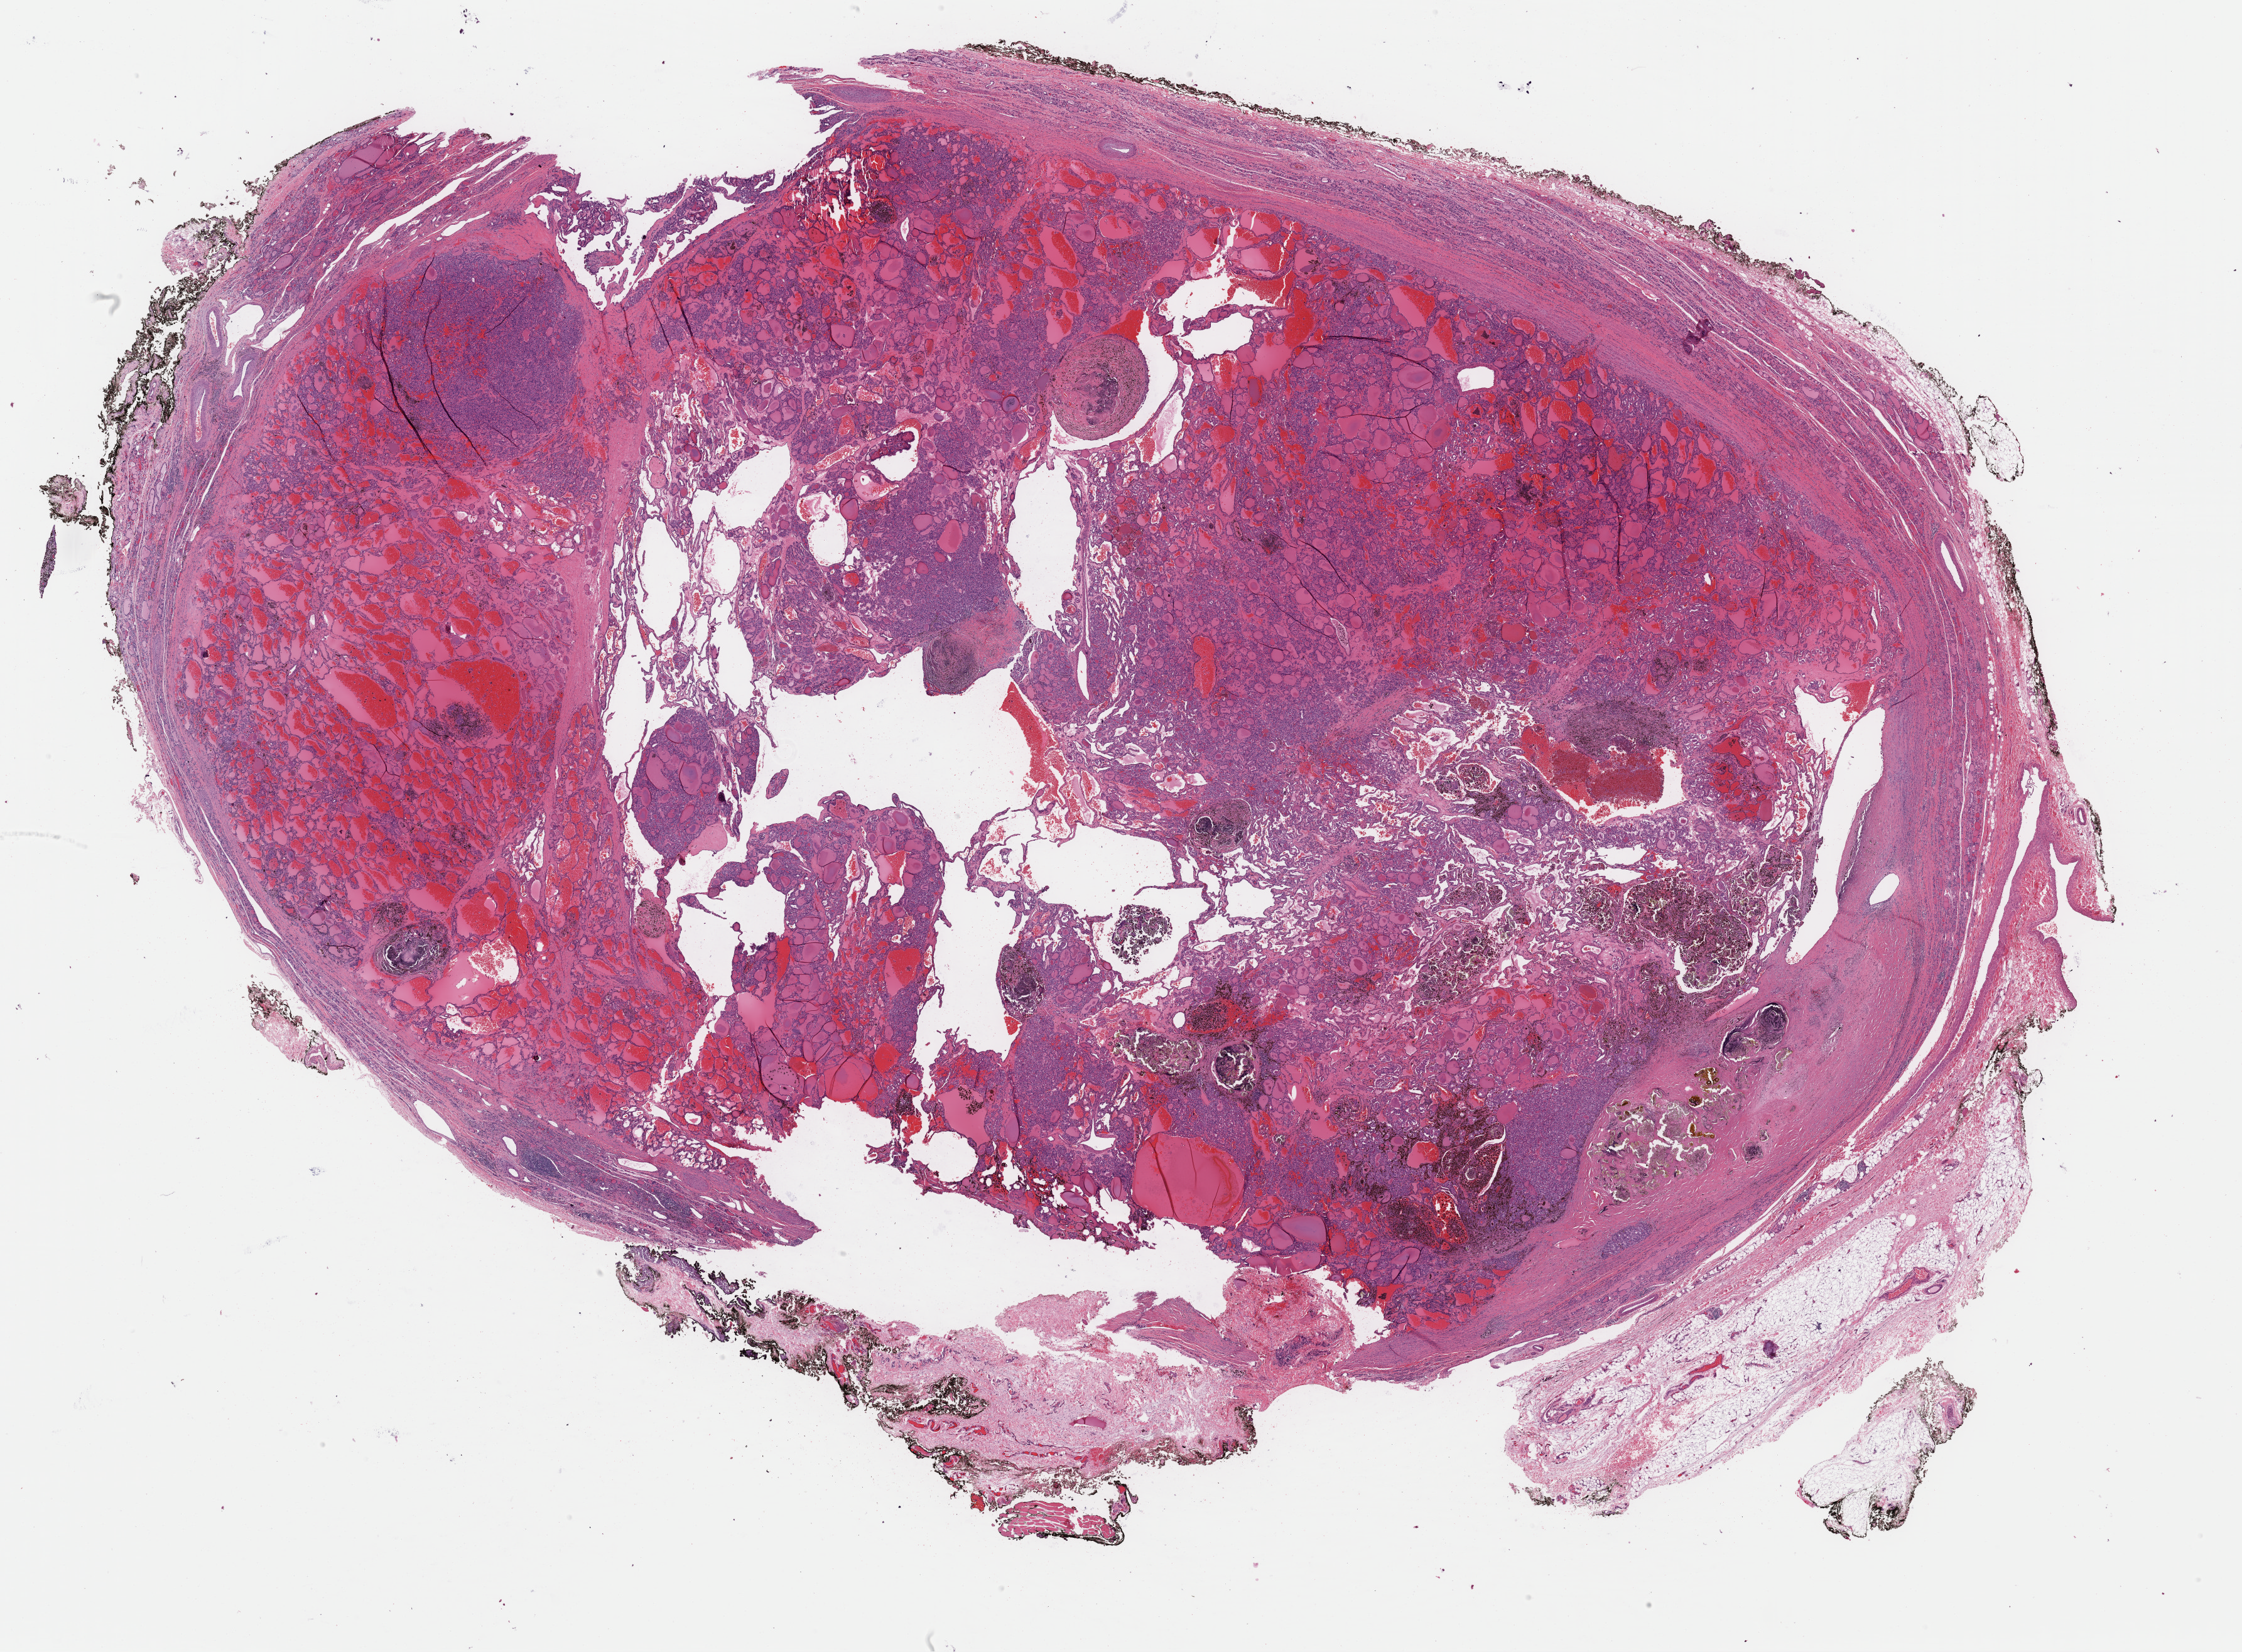
H&E whole-slide image, shown as a low-resolution overview of the whole scanned area (about 28.2 x 20.8 mm, from a 40x scan). Formalin-fixed paraffin-embedded (FFPE) diagnostic section. Sample: primary tumour, thyroid. Patient: male, age at initial diagnosis 36 years.
Diagnosis: Papillary carcinoma, follicular variant (thyroid gland).